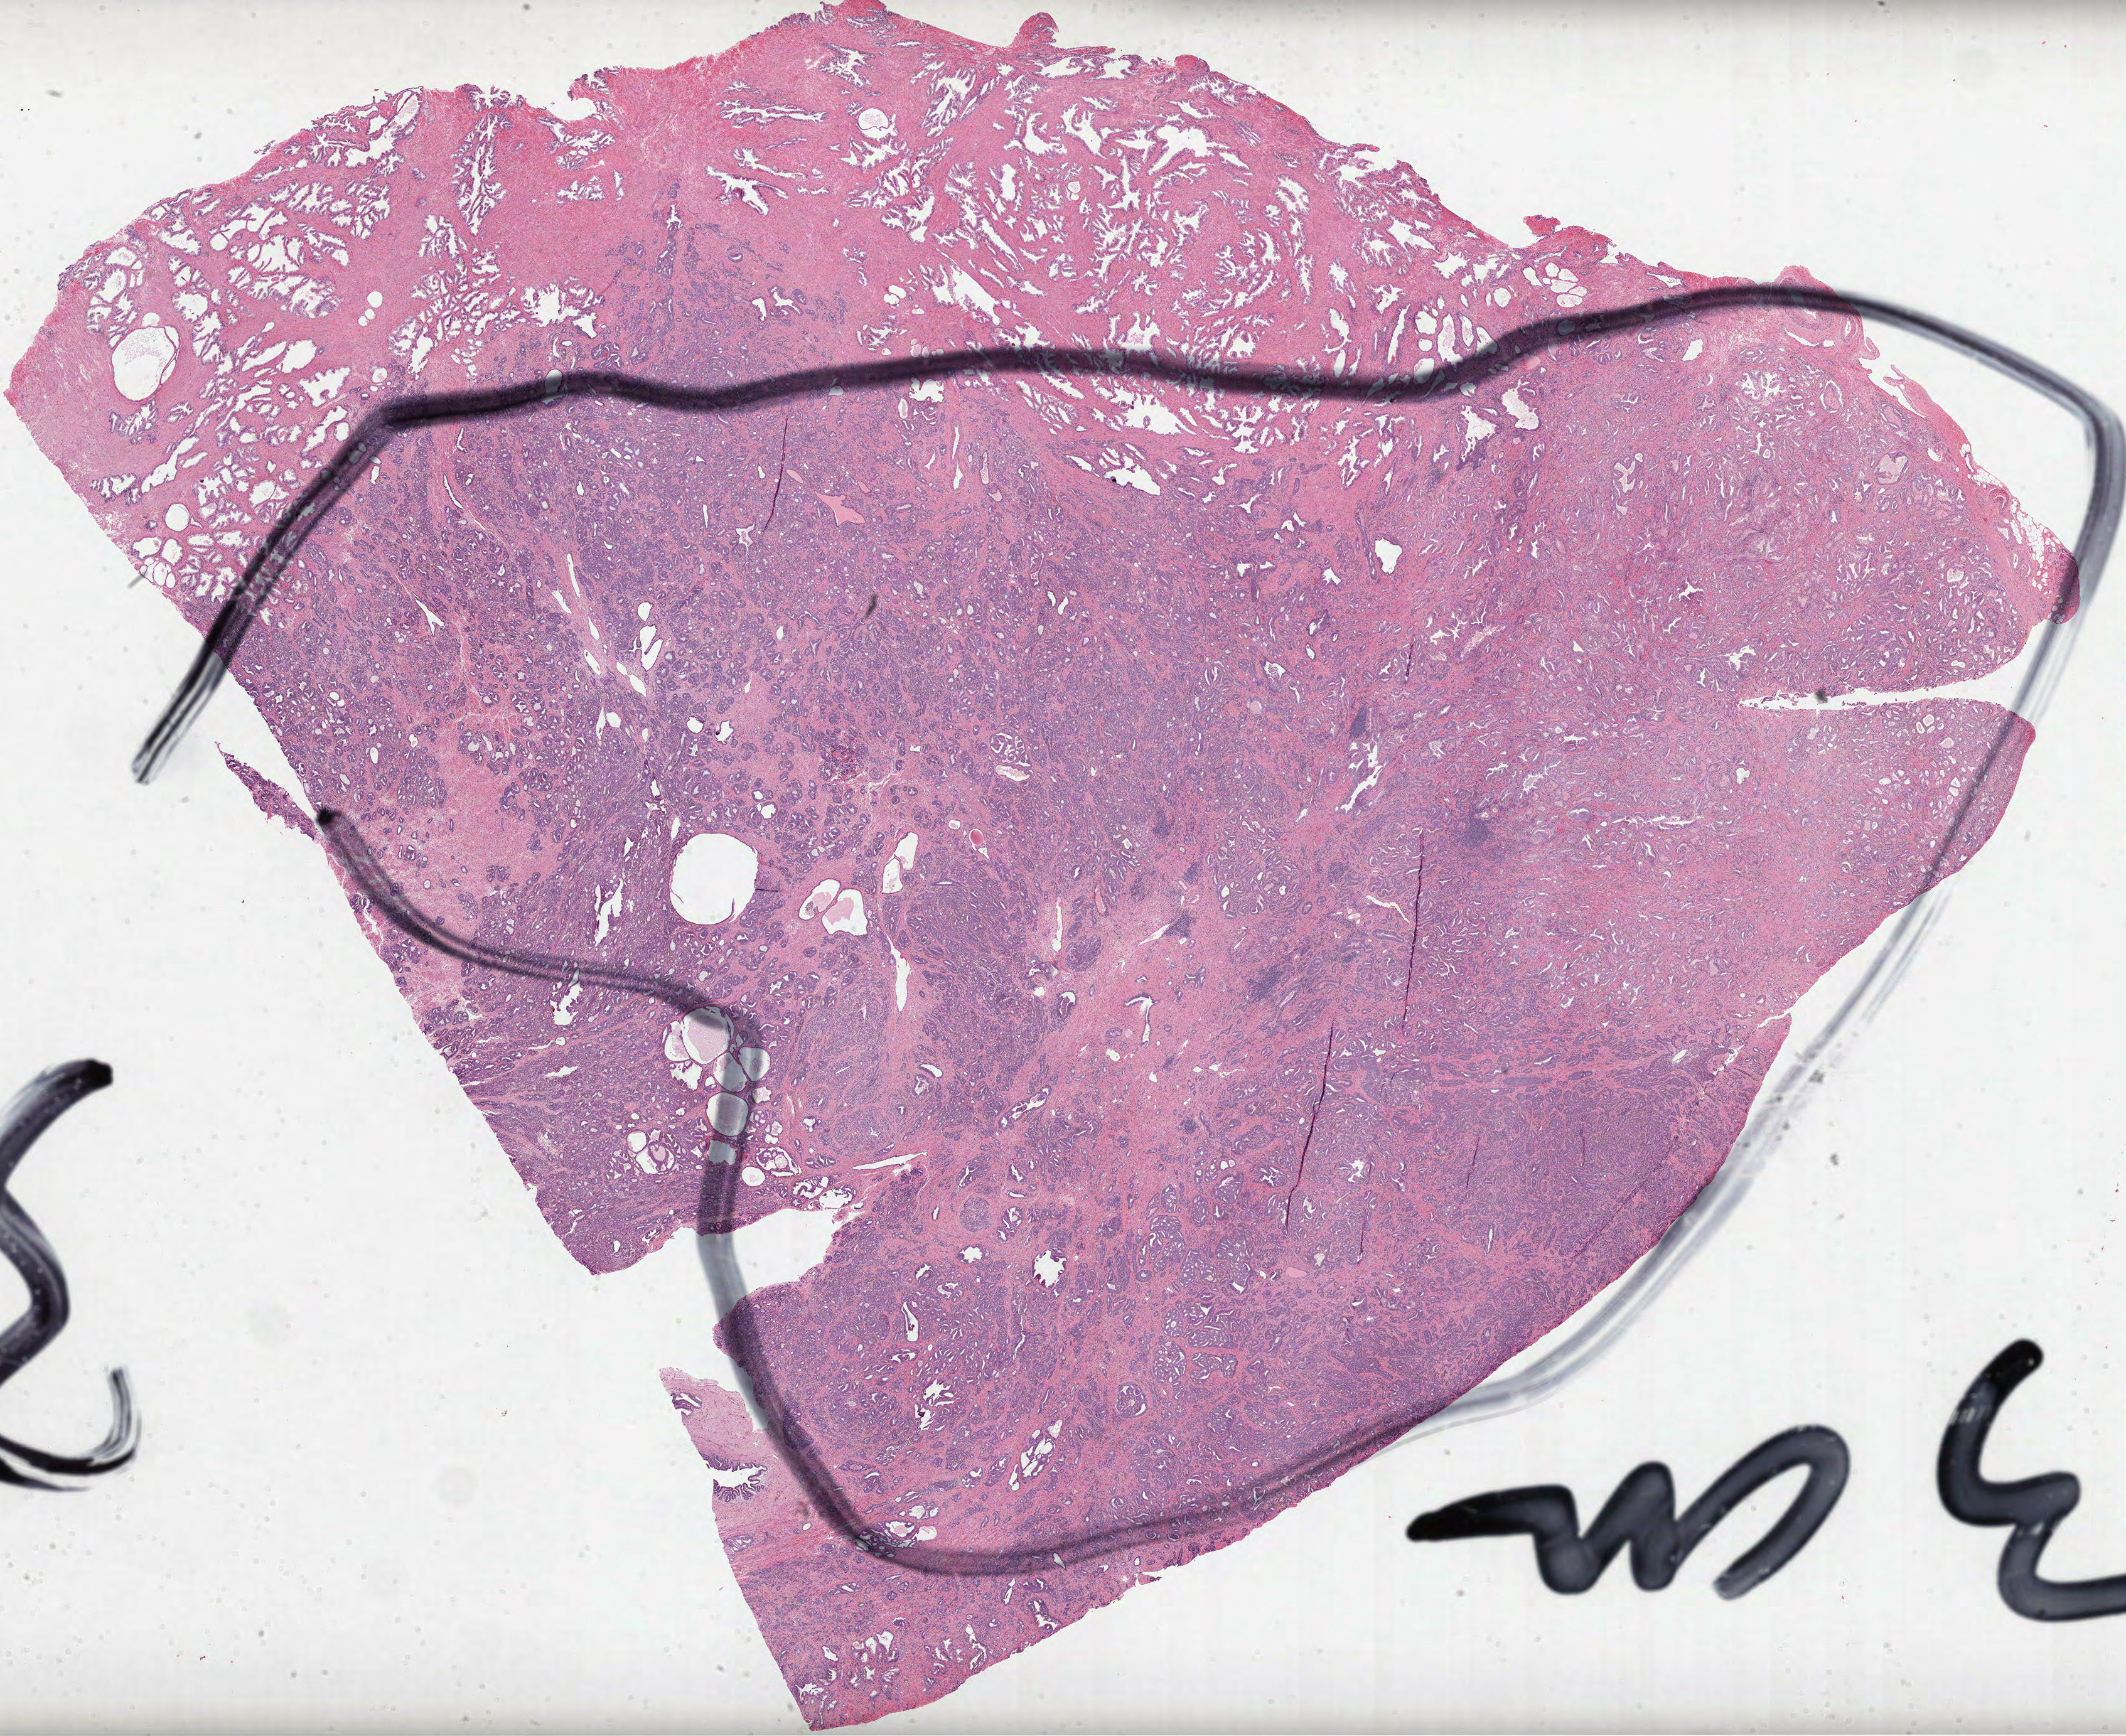
H&E-stained whole-slide image, whole scanned area (about 27.3 x 22.3 mm) shown as a low-resolution overview. Formalin-fixed paraffin-embedded (FFPE) diagnostic section. Prostate, primary tumour sample. Patient: male, age at initial diagnosis 61 years. Gleason score: 7 (4+3).
Laterality: bilateral. Lymph nodes positive (case pathology): 0 of 19 examined. Diagnosis: Acinar cell carcinoma (prostate gland).